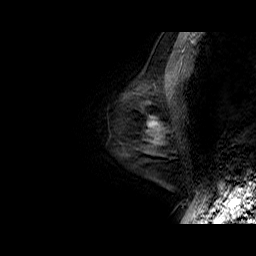
Breast MRI (dynamic contrast-enhanced), one sagittal slice. Position 13 of 50 along the scan axis. Dynamic contrast-enhanced series, time point 2 of 6 at this slice position (early post-contrast). 1.5 T. TE 6.5 ms, TR 32.9 ms. 4 mm slice thickness. 256 × 256 image matrix, field of view 200 × 200 mm. Female patient. From the clinical record (not read from this slice): setting: breast cancer imaged before/during neoadjuvant chemotherapy; receptor status: HR-positive, HER2-negative.
Annotated regions visible in this slice (semi-automatically segmented with operator editing):
- analysis volume of interest (the breast-tissue region the enhancement analysis was run in; not a lesion): box from (x=125, y=75) to (x=179, y=149) px
- tumour enhancement mask (voxels above the 100 % enhancement threshold inside the analysis volume of interest): (x=147, y=117)–(x=158, y=128)